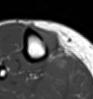
MRI of an extremity soft-tissue mass, one axial slice; slice 19 of 54 in the series (ordered by position); MR volume resampled by the dataset authors to the PET/CT grid (not the native acquisition matrix); 93 × 99 image matrix. Female patient. From the clinical record (not read from this slice): histological type: undifferentiated – high grade; grade: high; site of the primary tumour: right thigh.
Structures marked on this image (expert contour drawn on MRI and transferred to this co-registered scan by the dataset authors):
- gross tumour volume (mass): box from (x=38, y=29) to (x=60, y=58) px